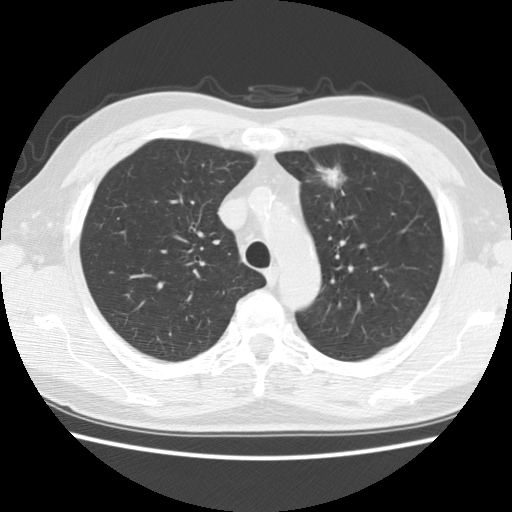
Low-dose screening chest CT, one axial slice. Slice 127 of 172 in the series (ordered by position). Lung window (W 1500 / L -600 HU). 512 × 512 image matrix.
Structures marked on this image (outlined manually by an expert reader):
- lesion 1 (tumor, upper lobe of left lung): bounding box <316,165,346,188> (left, top, right, bottom; pixels)